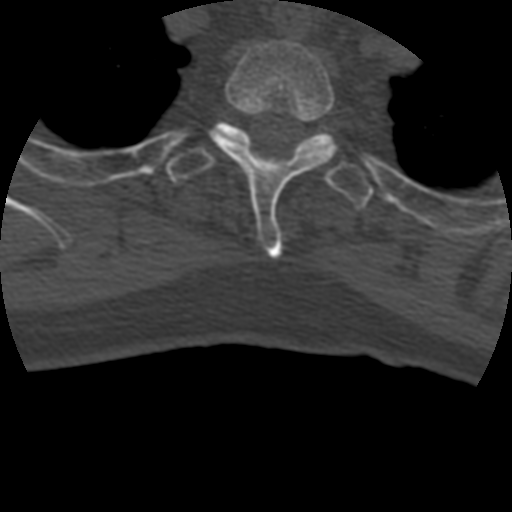
CT including the spine, one axial slice; slice 363 of 399 in the series (ordered by position); 120 kVp; bone window (W 1800 / L 400 HU); 1.25 mm slice thickness; 512 × 512 image matrix. Patient age 69 years. Case-level facts recorded for this patient, not image findings: primary cancer: prostate.
Annotated regions visible in this slice (semi-automatic segmentation, software-assisted and operator-edited):
- T2 vertebra: bounding box (x1, y1, x2, y2) in pixels: (210, 40, 336, 258)
- T3 vertebra: (167, 121, 374, 210)